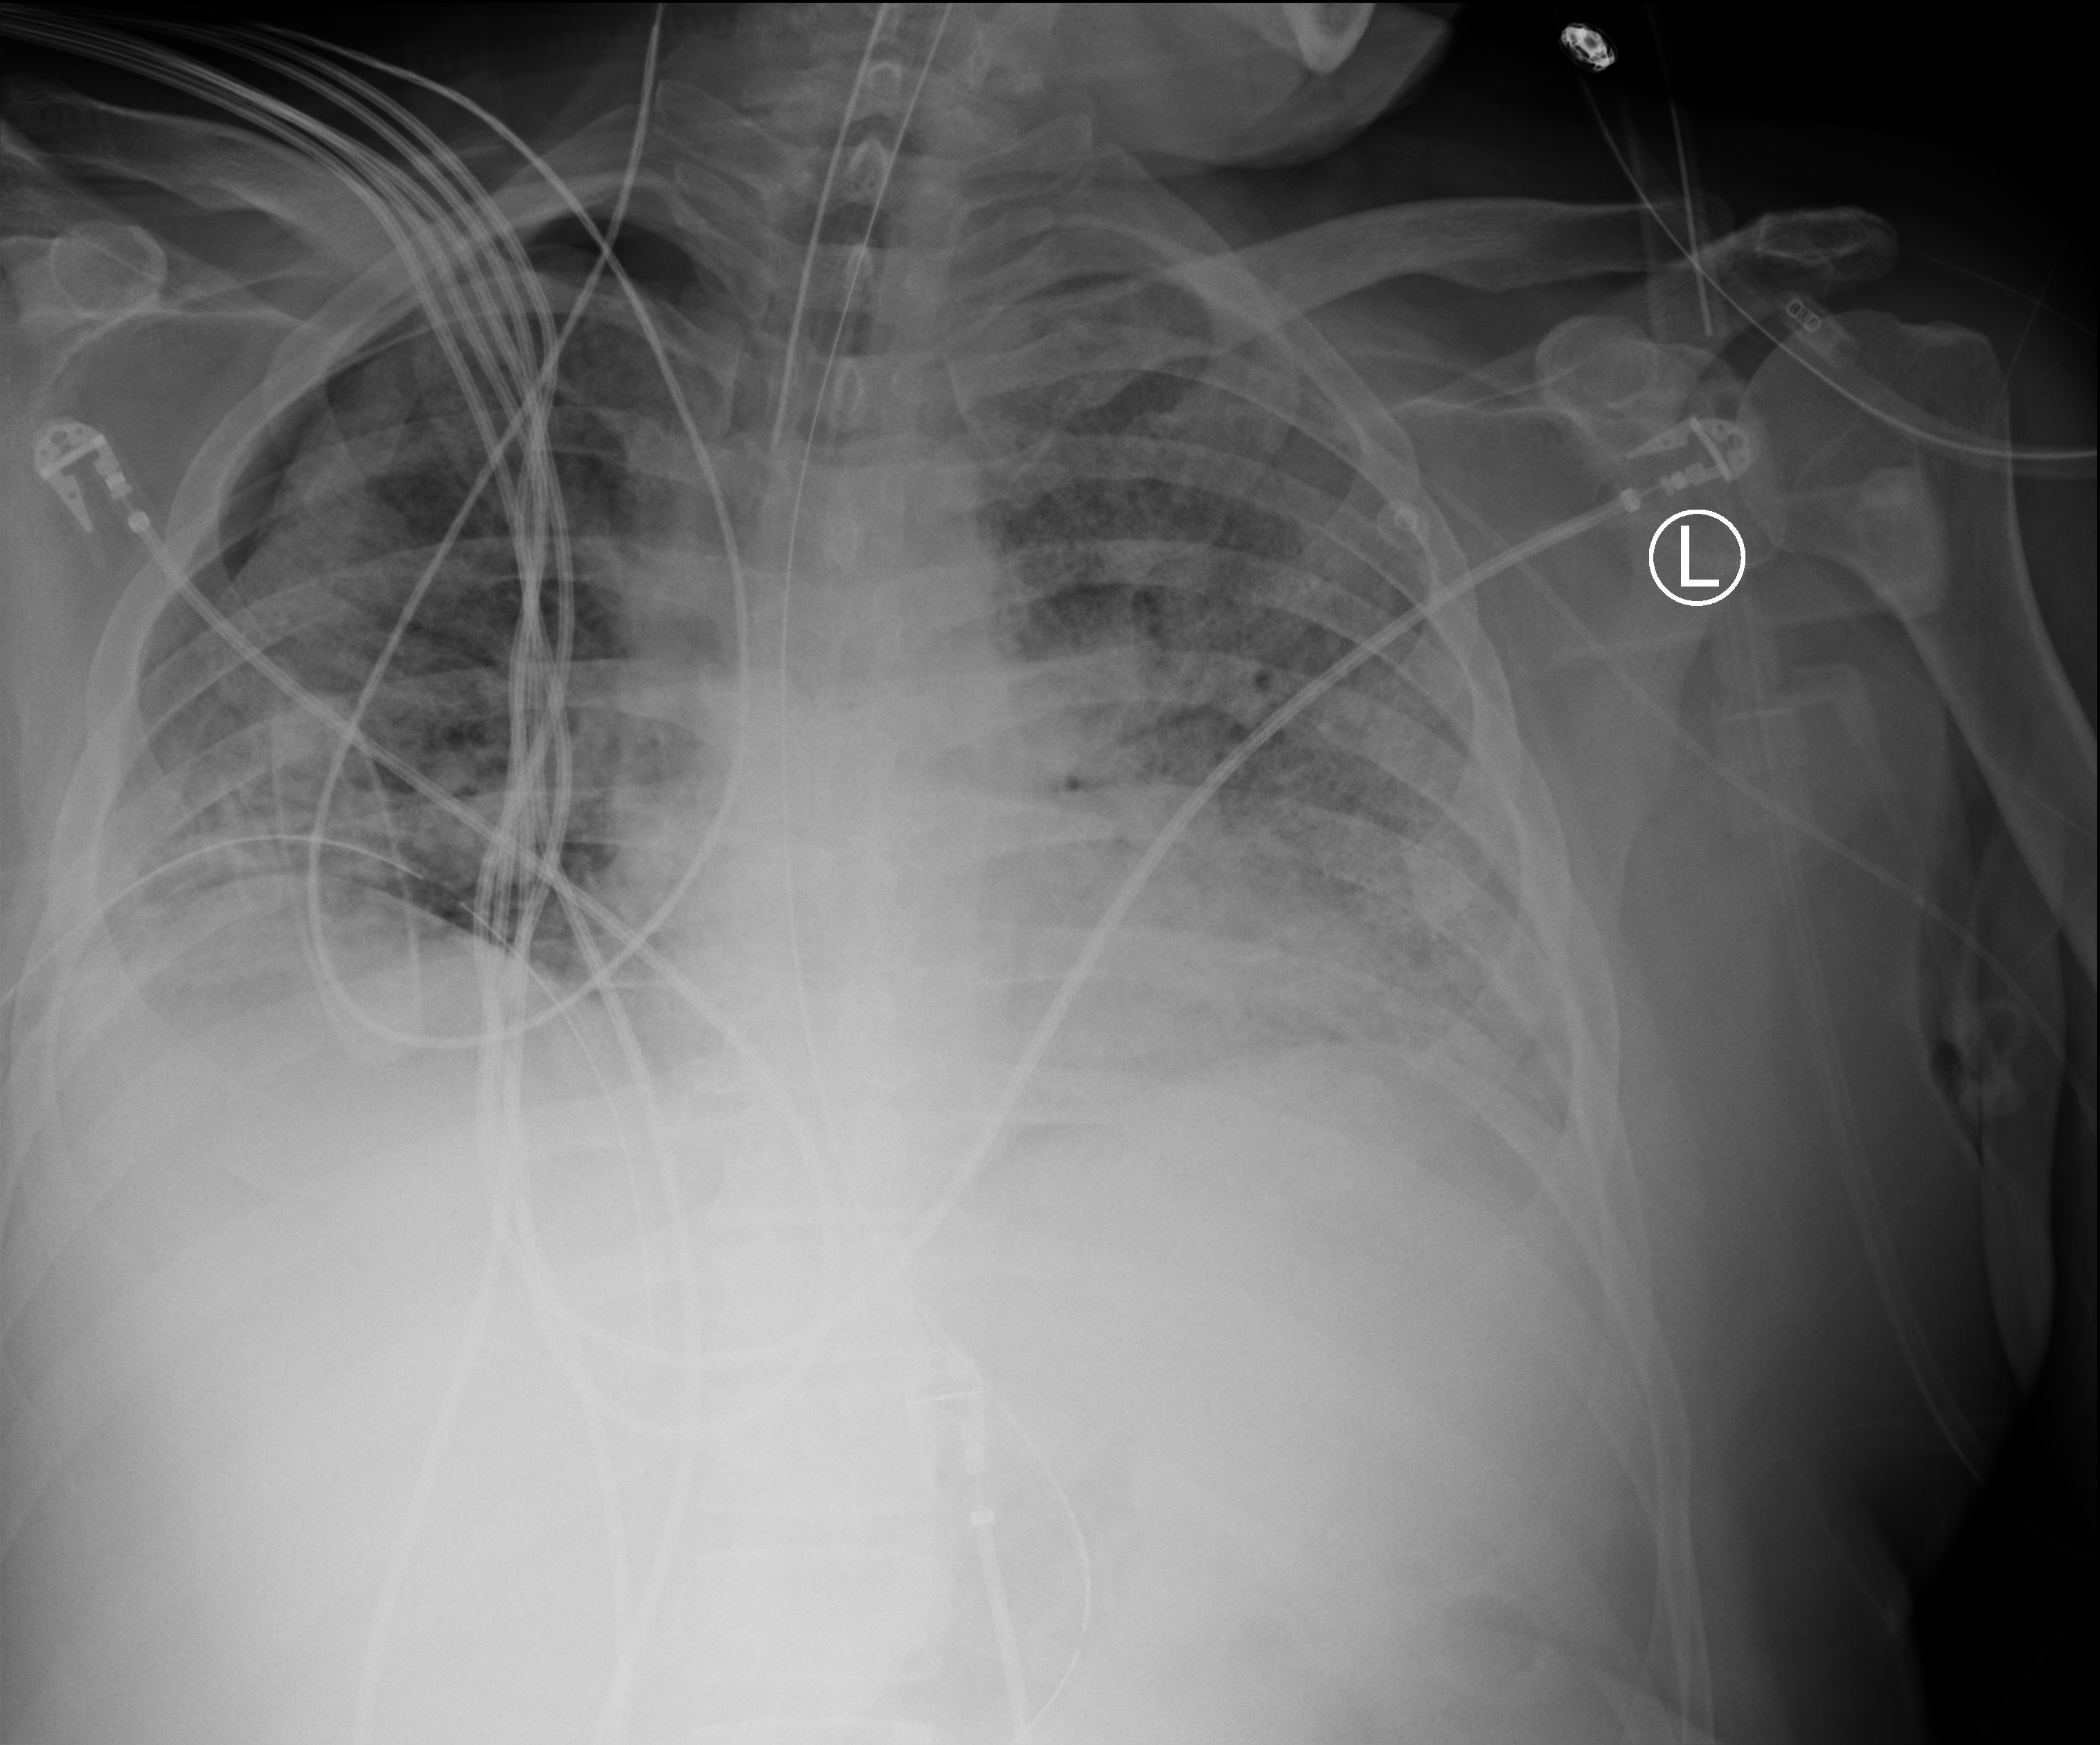
Bedside chest radiograph (computed radiography); anteroposterior (AP) projection. Patient hospitalised with COVID-19; male, aged 18–59 years.
Admission-level facts for this patient (not findings on this image; timing relative to this image not recorded): admitted to intensive care during this hospital stay: yes.